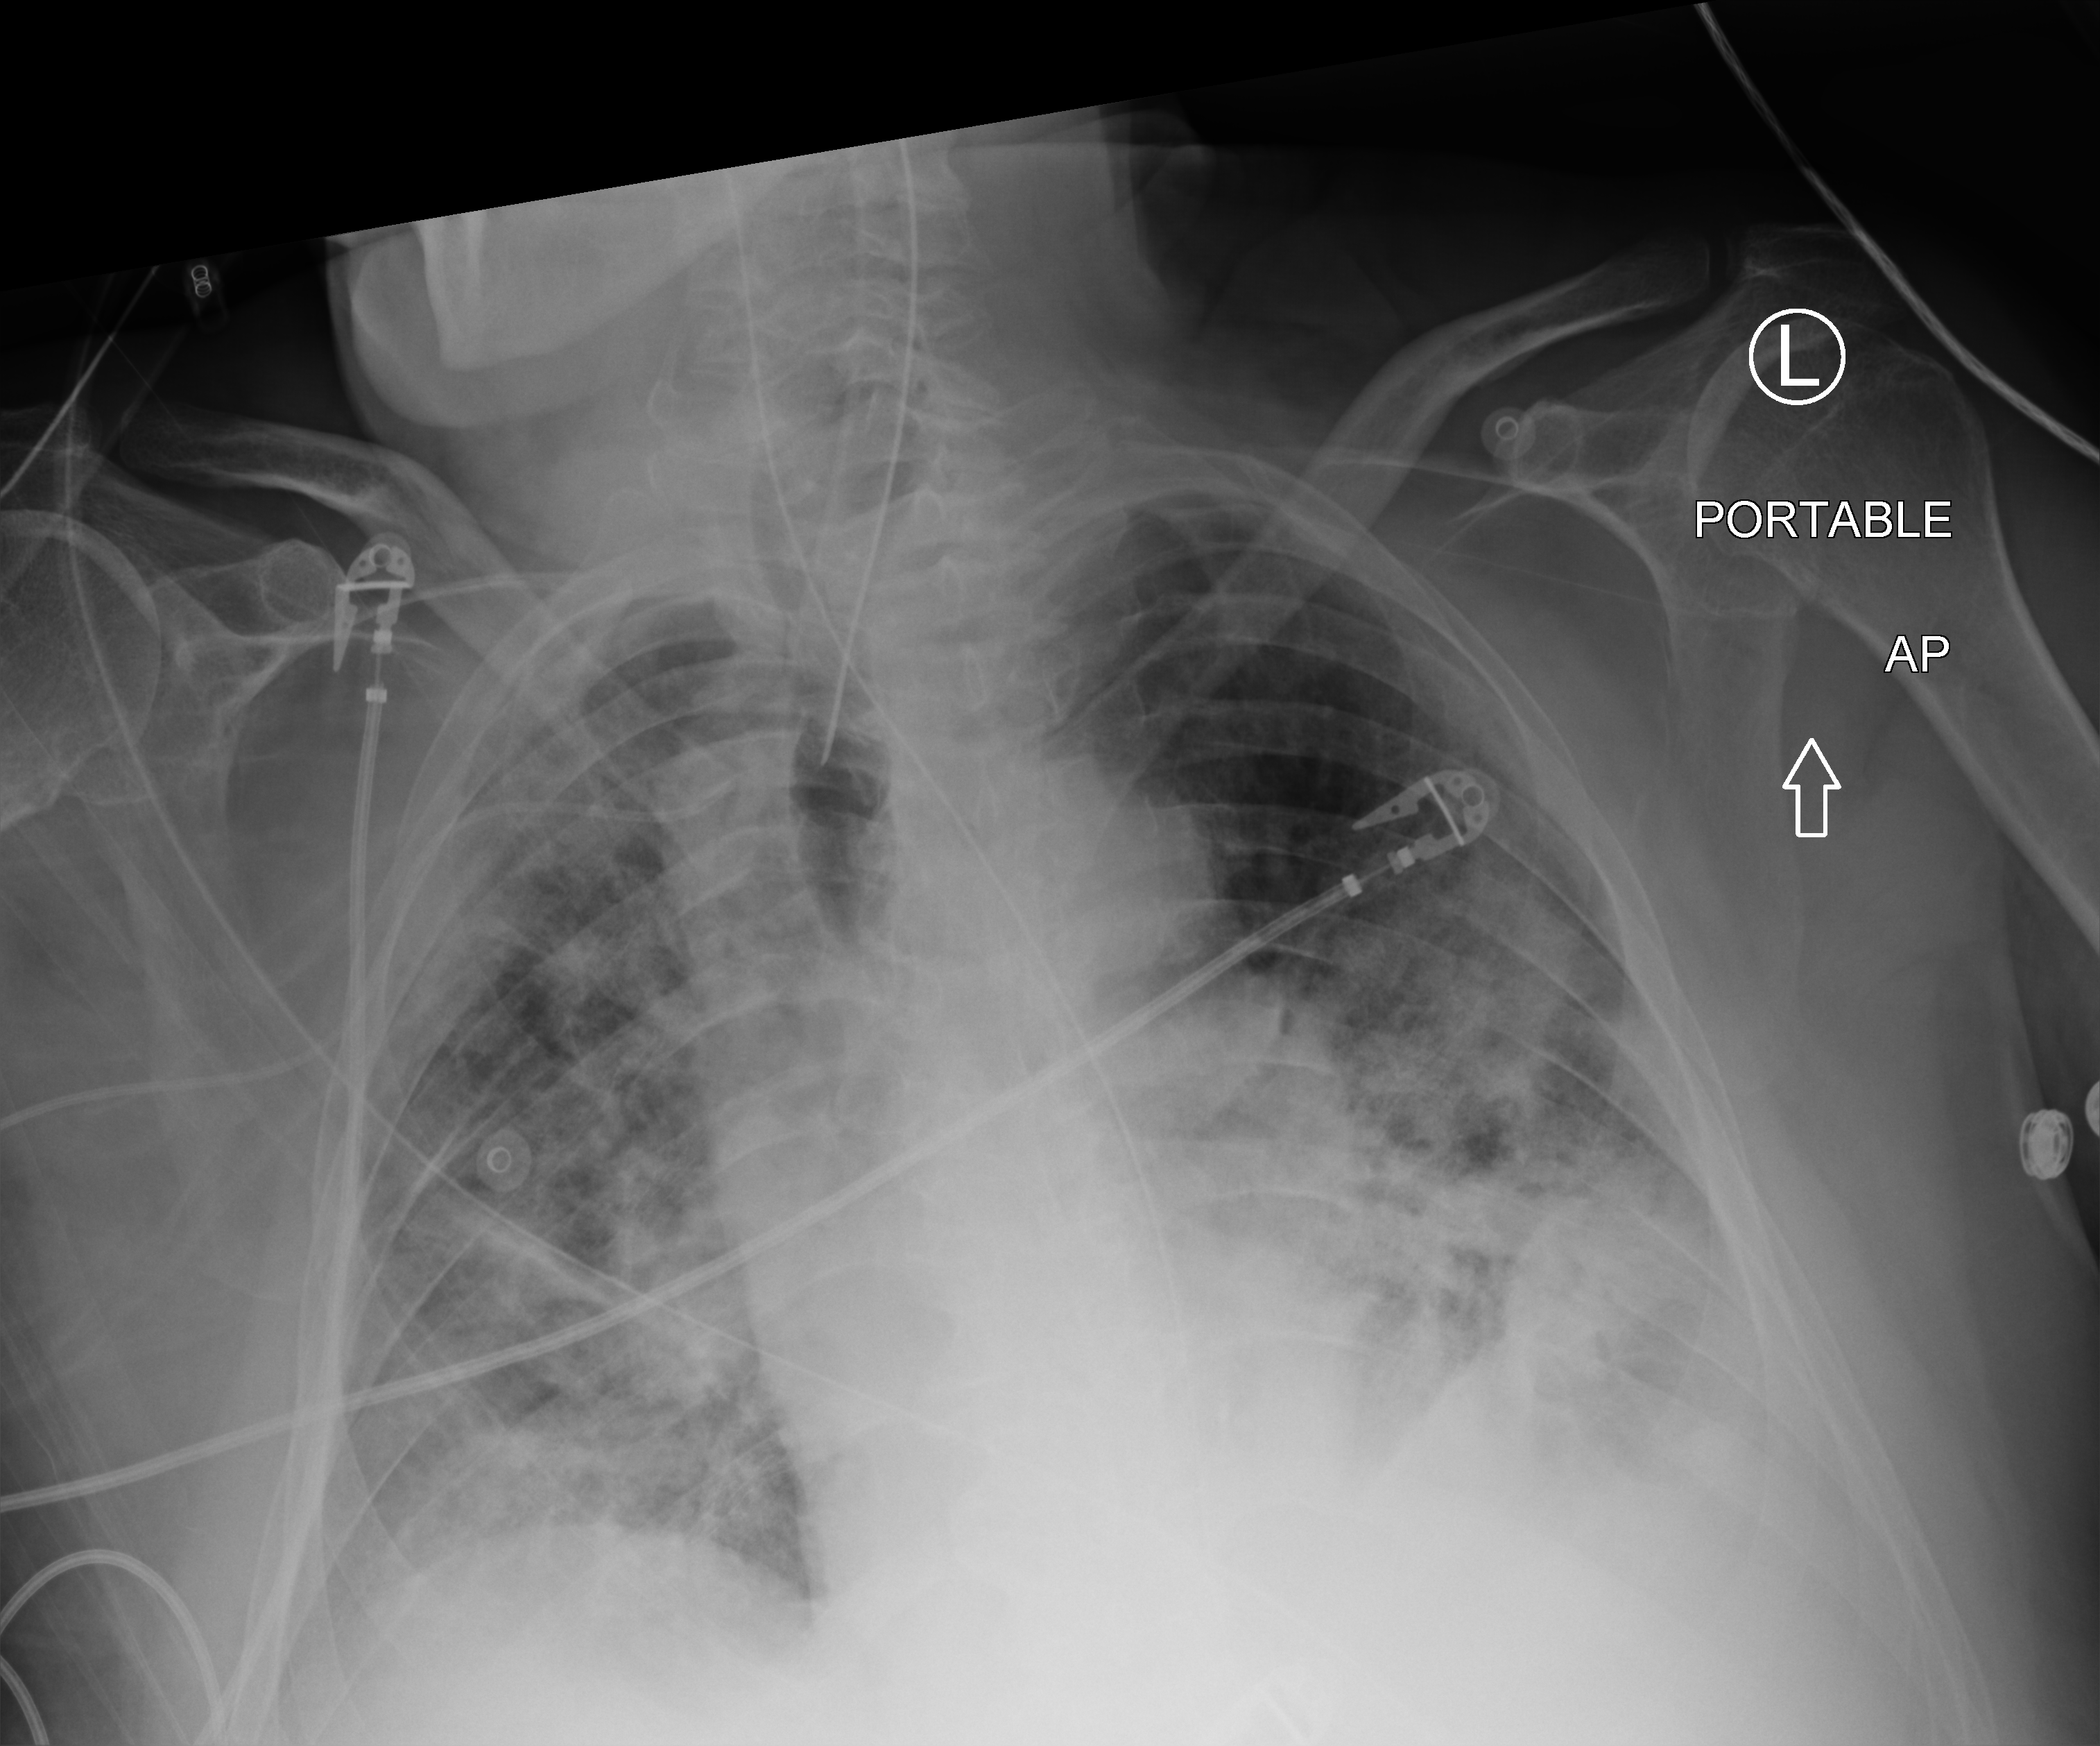
Chest X-ray (portable). Male patient hospitalised with COVID-19, age 60–74 years.
Hospital-stay facts (about this admission, not read from this image; timing relative to this image not recorded):
- hypertension (admission record): no
- mechanically ventilated during this hospital stay: yes
- length of hospital stay: 24 days